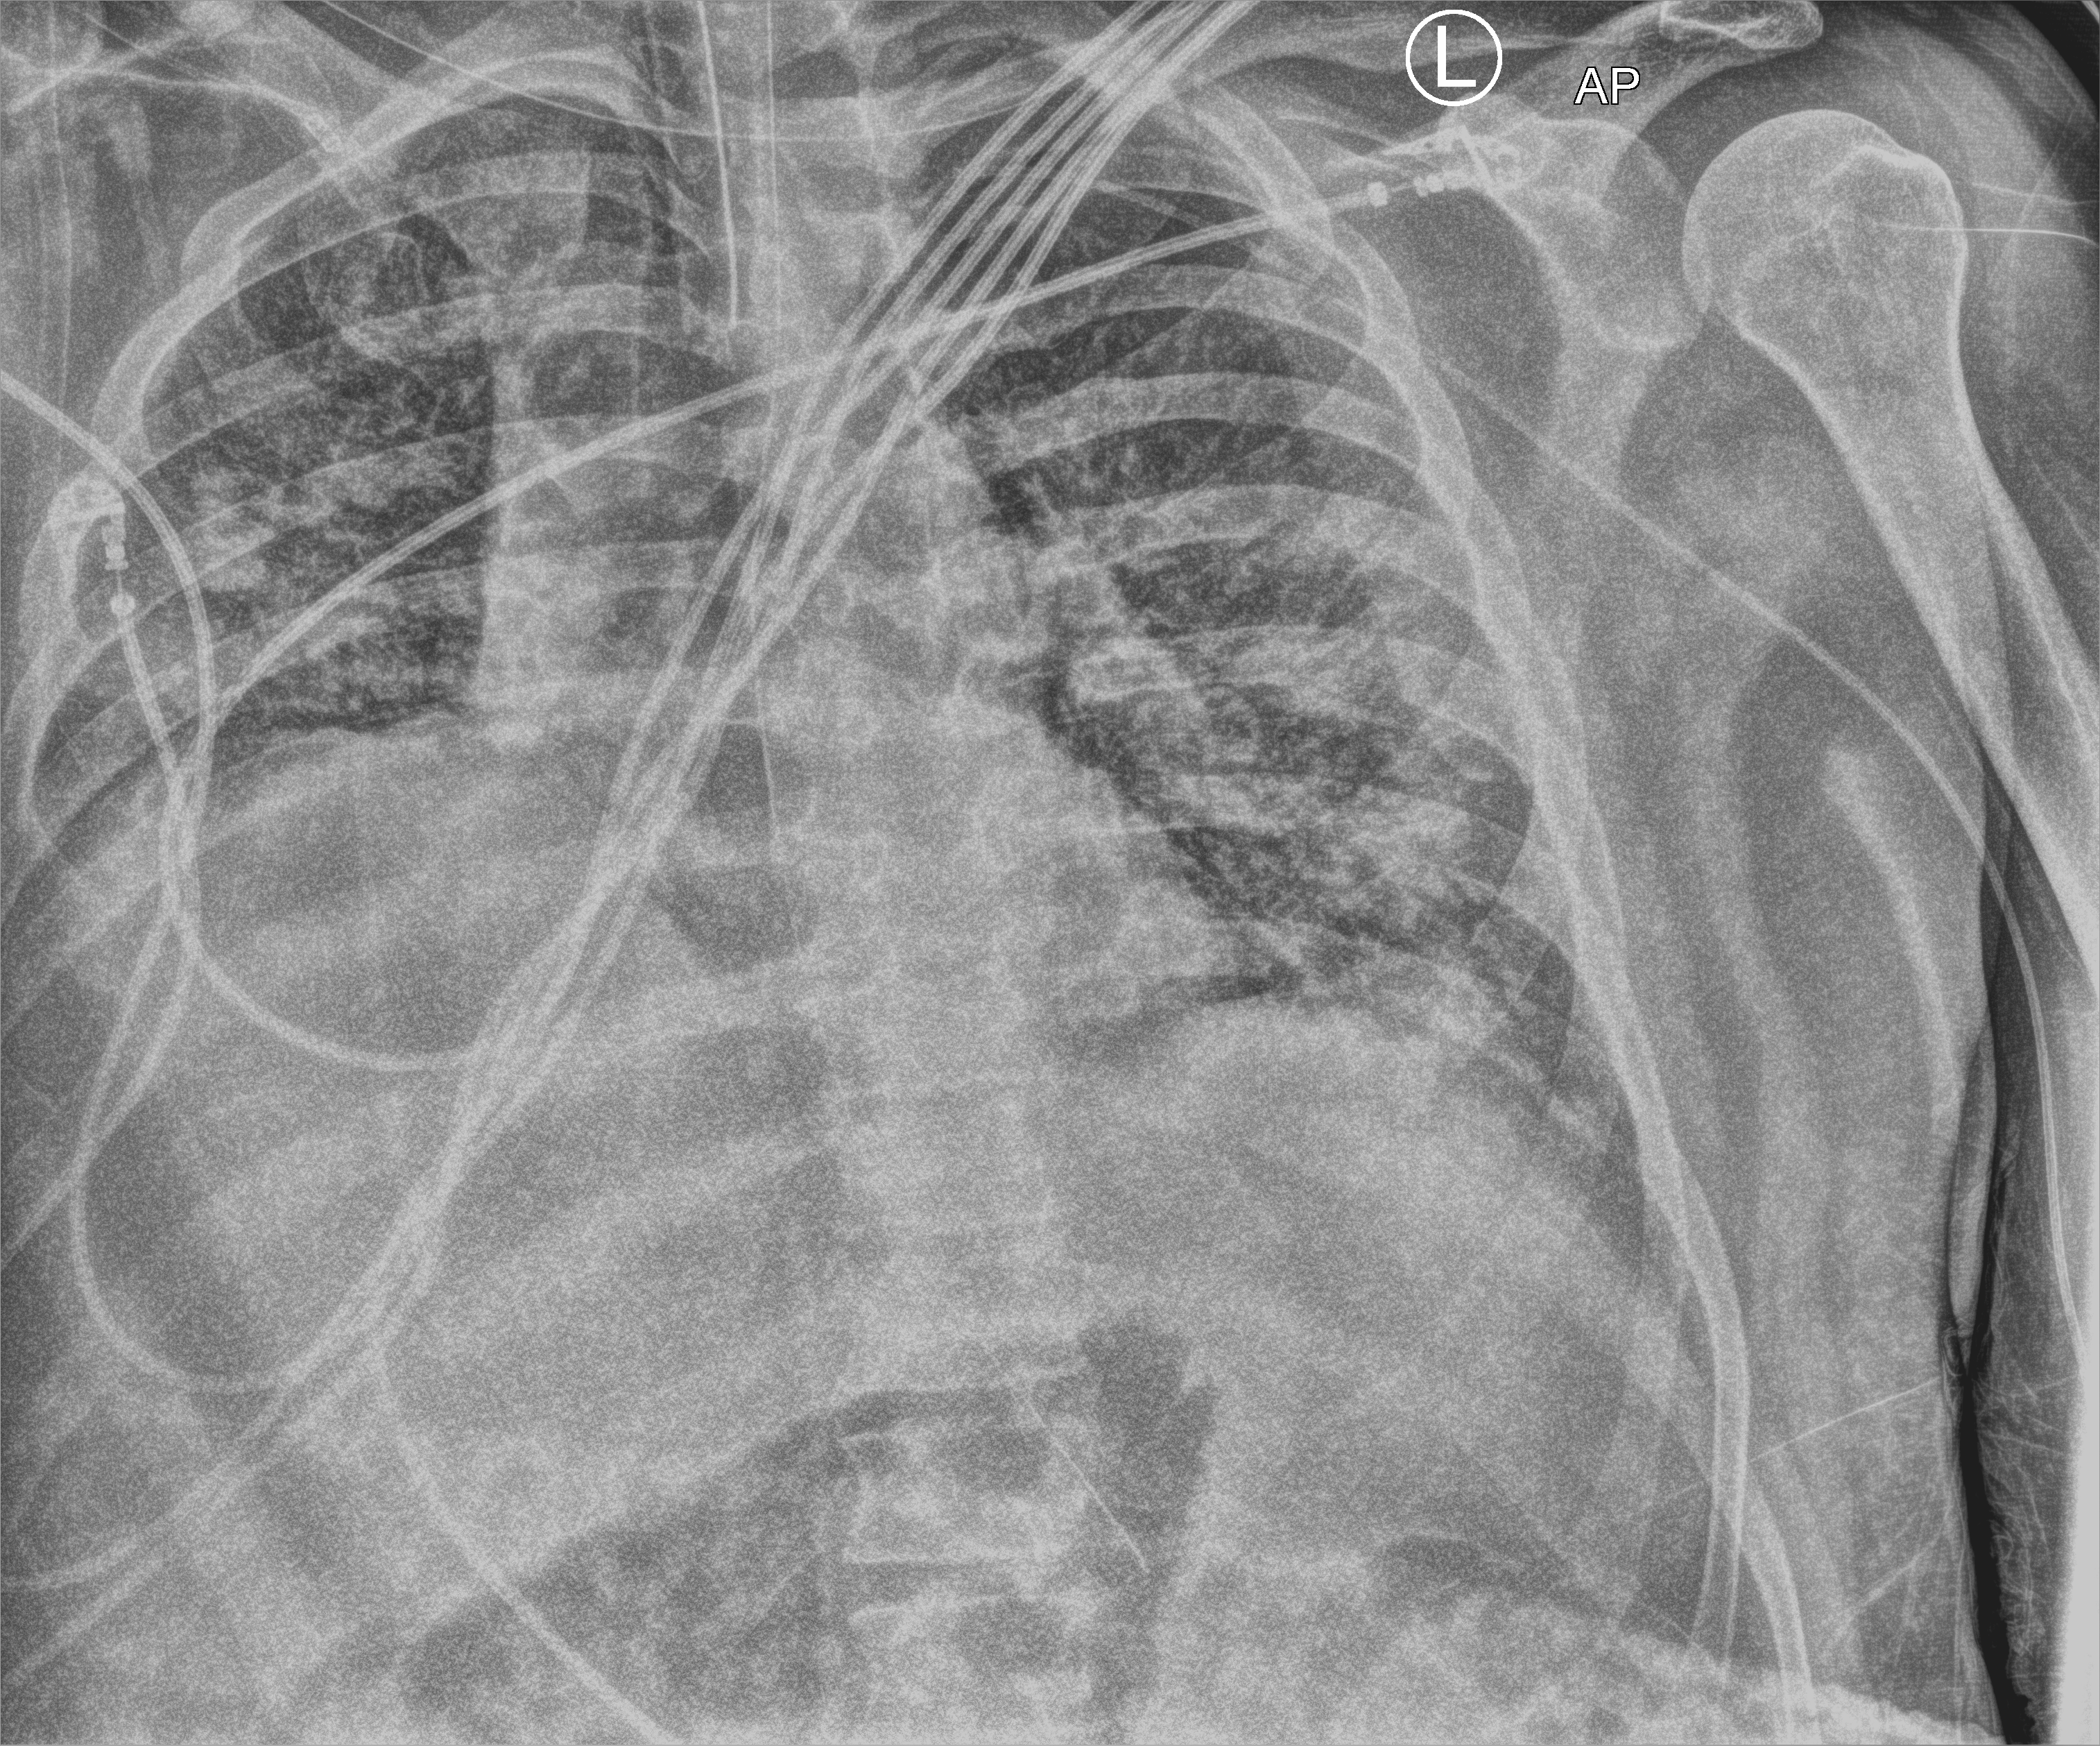
Chest X-ray (portable), anteroposterior (AP) projection. Patient hospitalised with COVID-19; male, aged 18–59 years.
Hospital-stay facts (about this admission, not read from this image; timing relative to this image not recorded): mechanically ventilated during this hospital stay: yes.